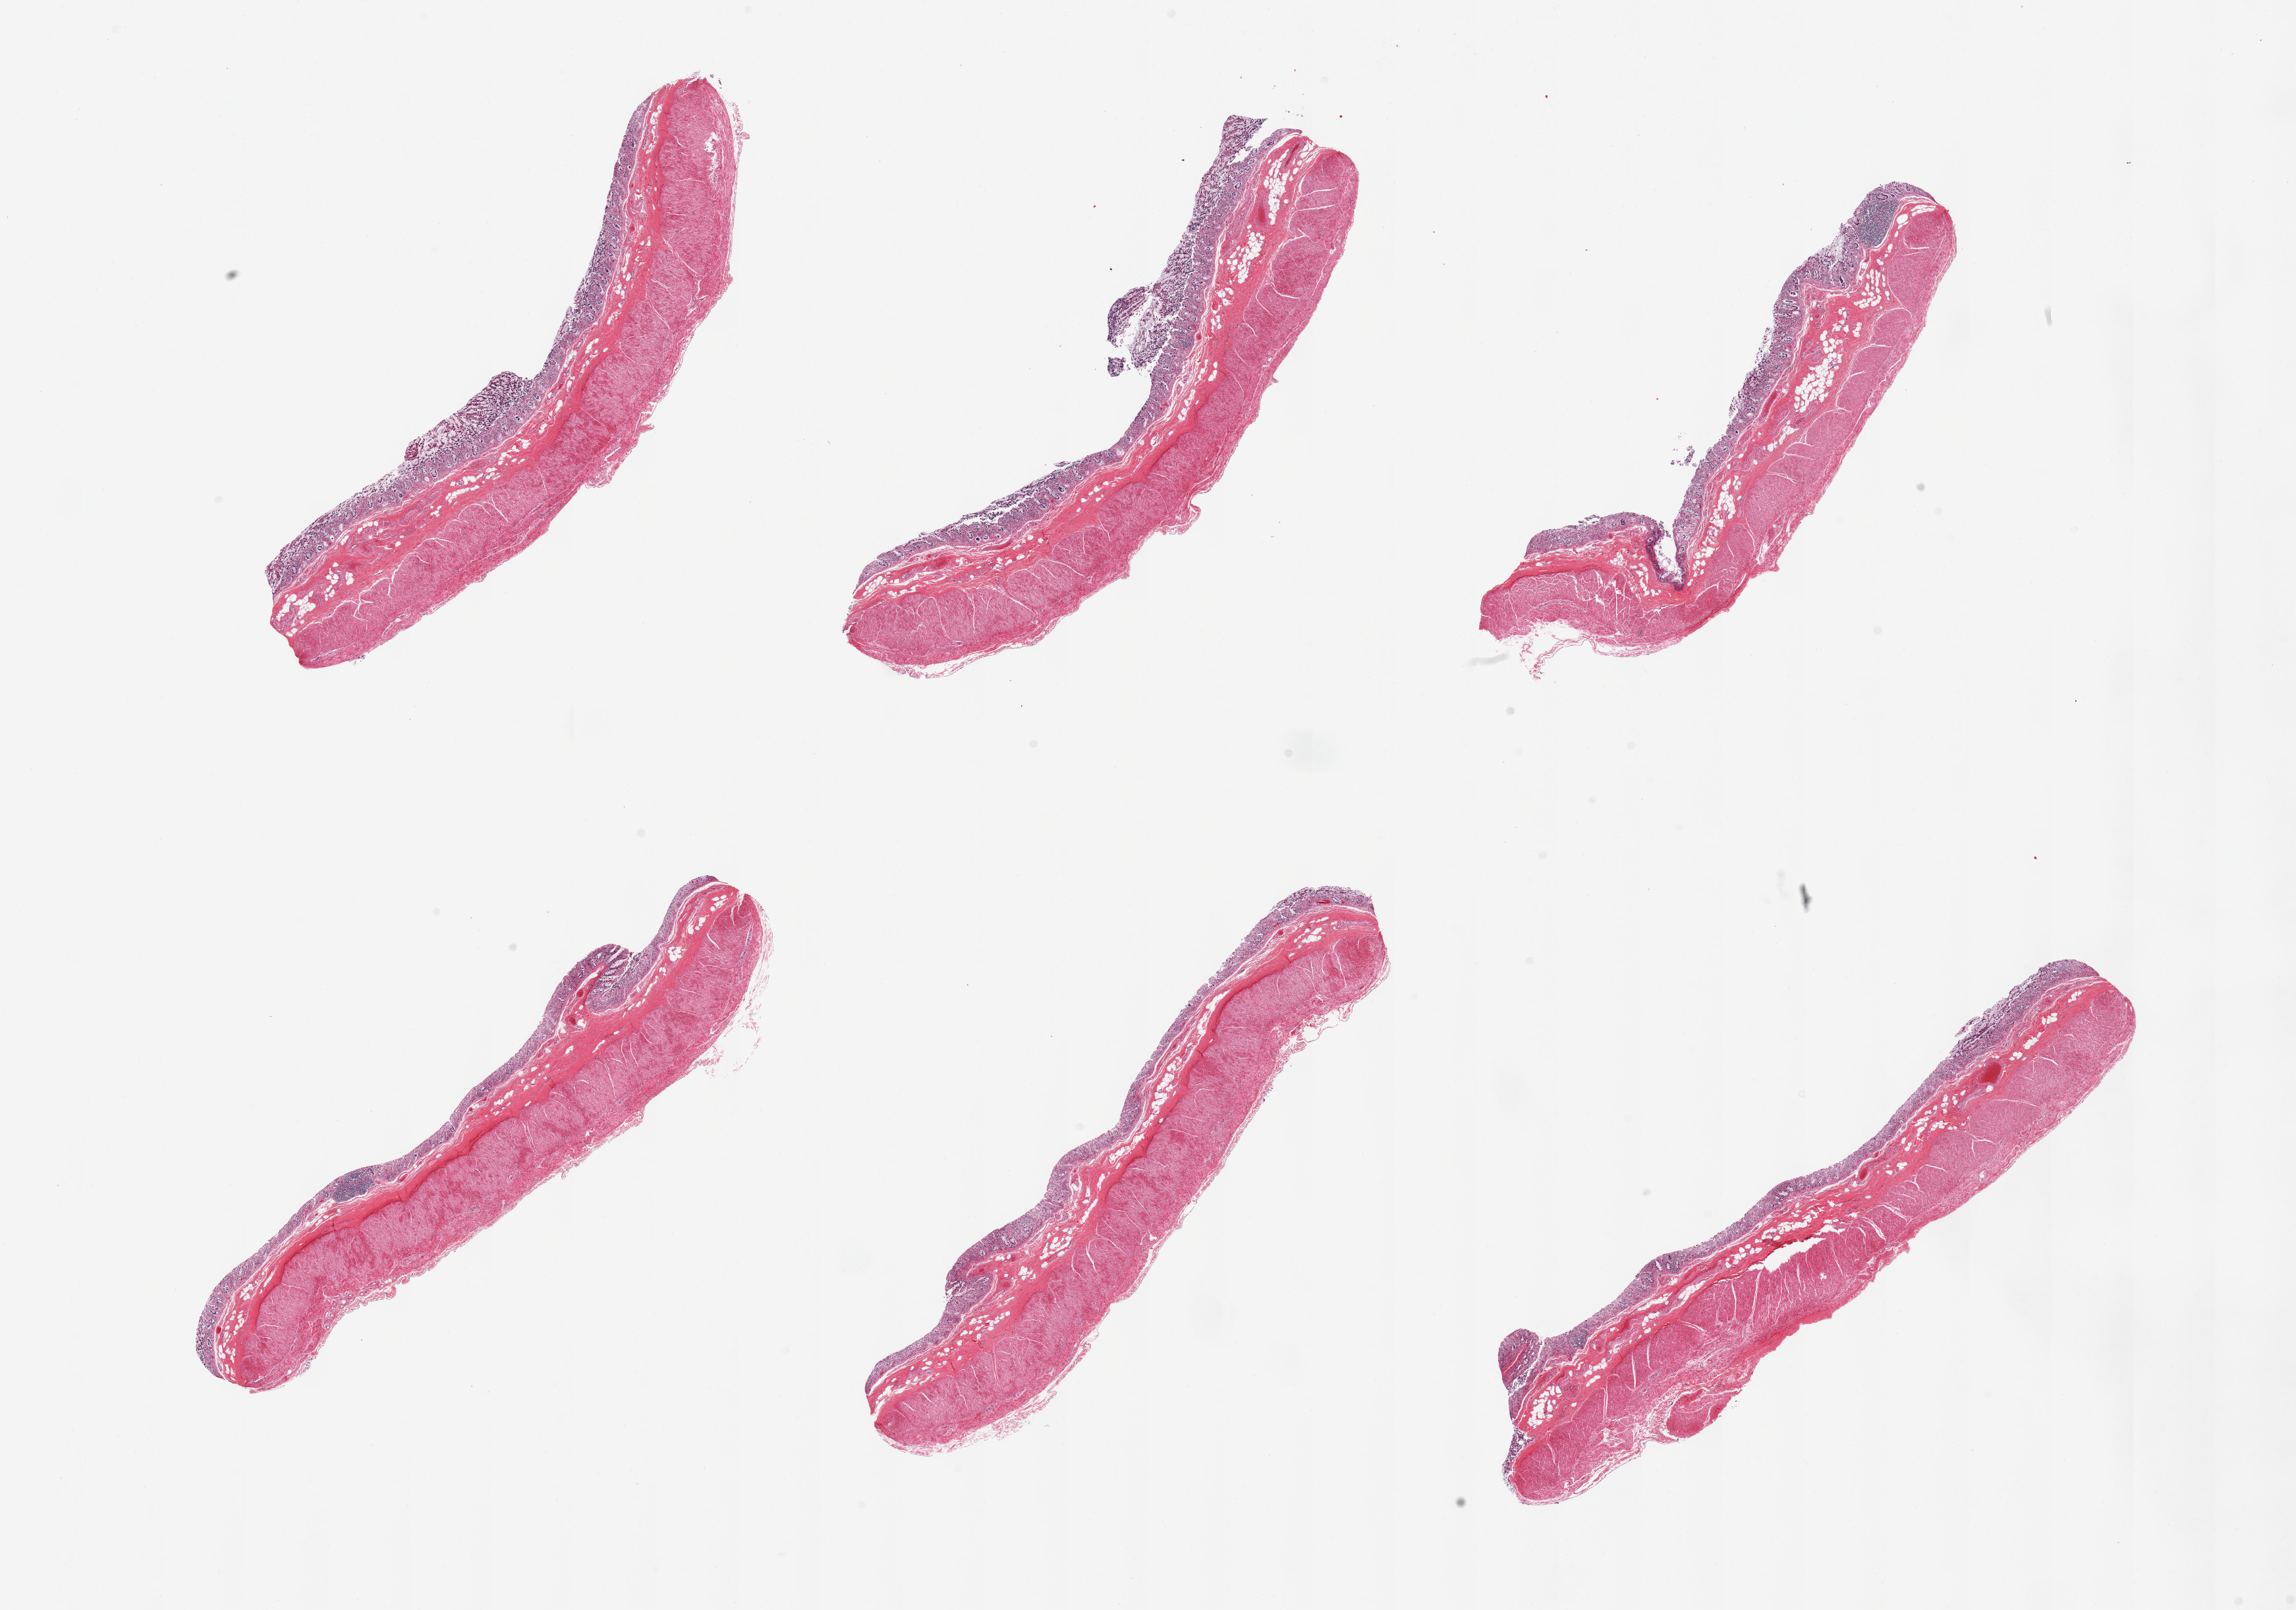
Digitized haematoxylin and eosin-stained section, brightfield, low-resolution overview of the scanned area, about 27.6 x 19.3 mm (acquisition: 20x scan); PAXgene-fixed paraffin-embedded (PFPE) section; sampled site (target tissue): transverse colon; tissue donor sample. Male donor.
- pathologist's review note for this sample: 6 pieces; full thickness sections, moderate to severe autolysis